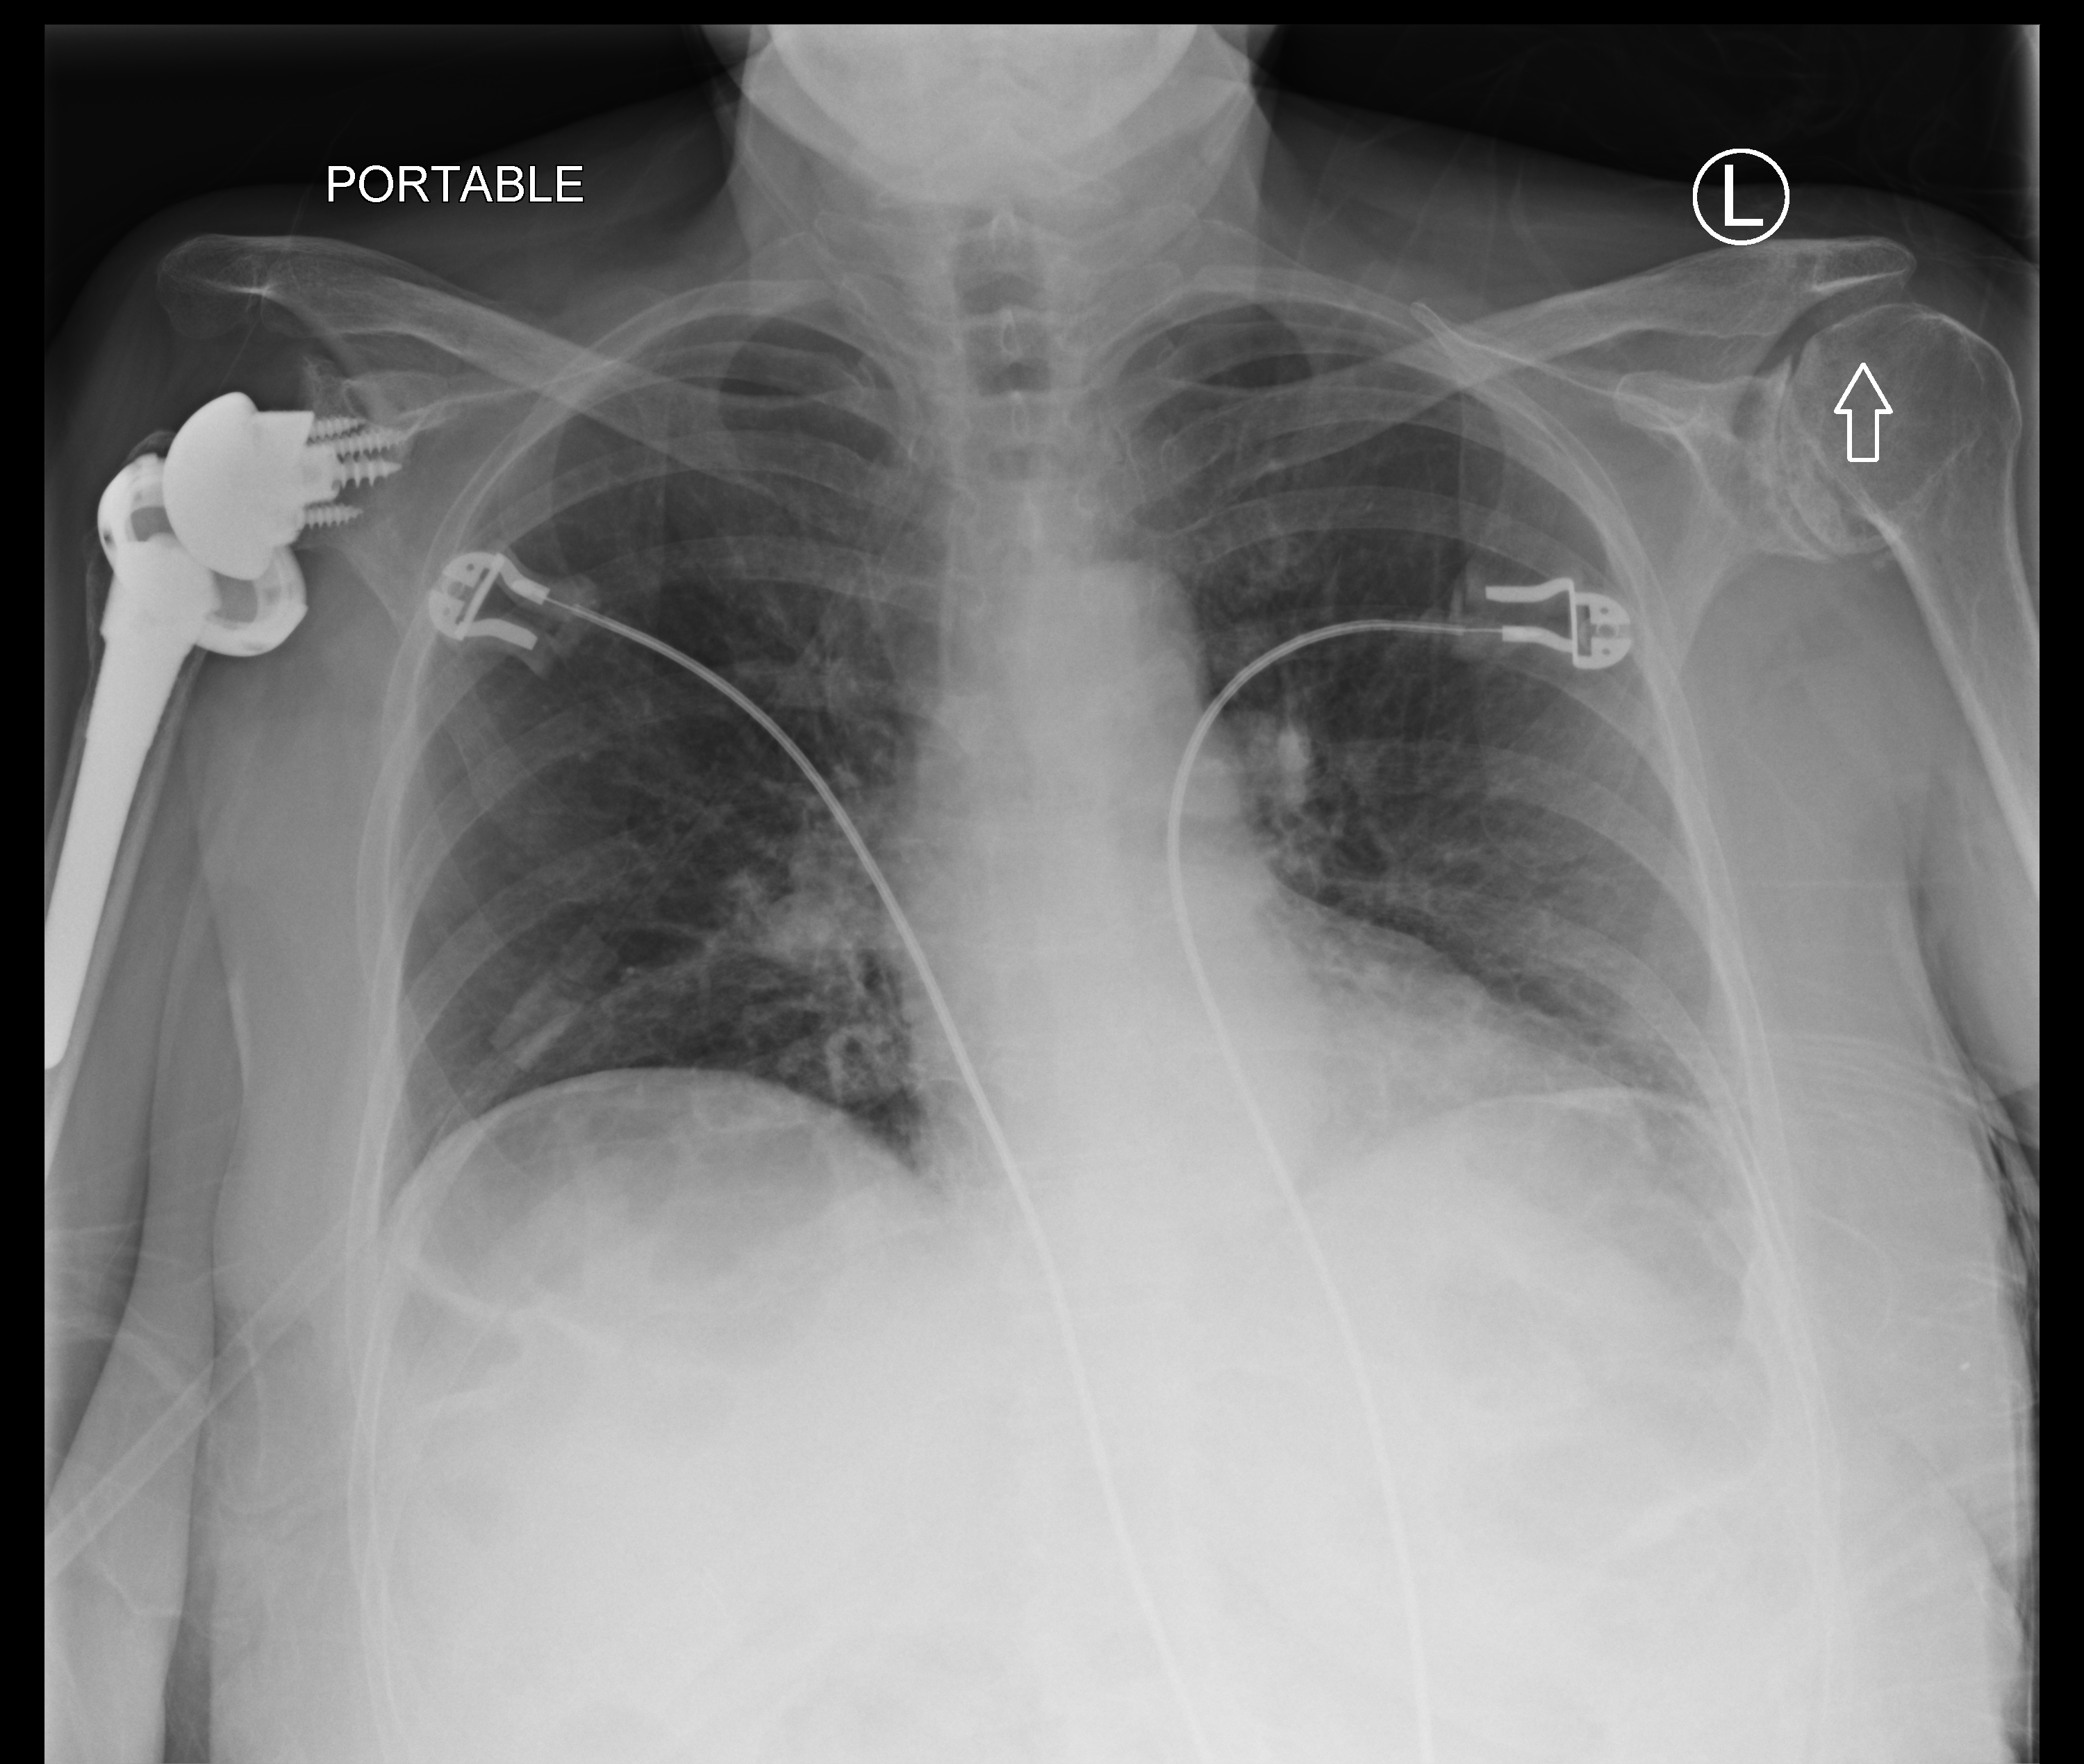
Bedside chest radiograph (computed radiography); anteroposterior (AP) projection. Female patient hospitalised with COVID-19, age 60–74 years.
Admission-level facts for this patient (not findings on this image; timing relative to this image not recorded): admitted to intensive care during this hospital stay: yes.